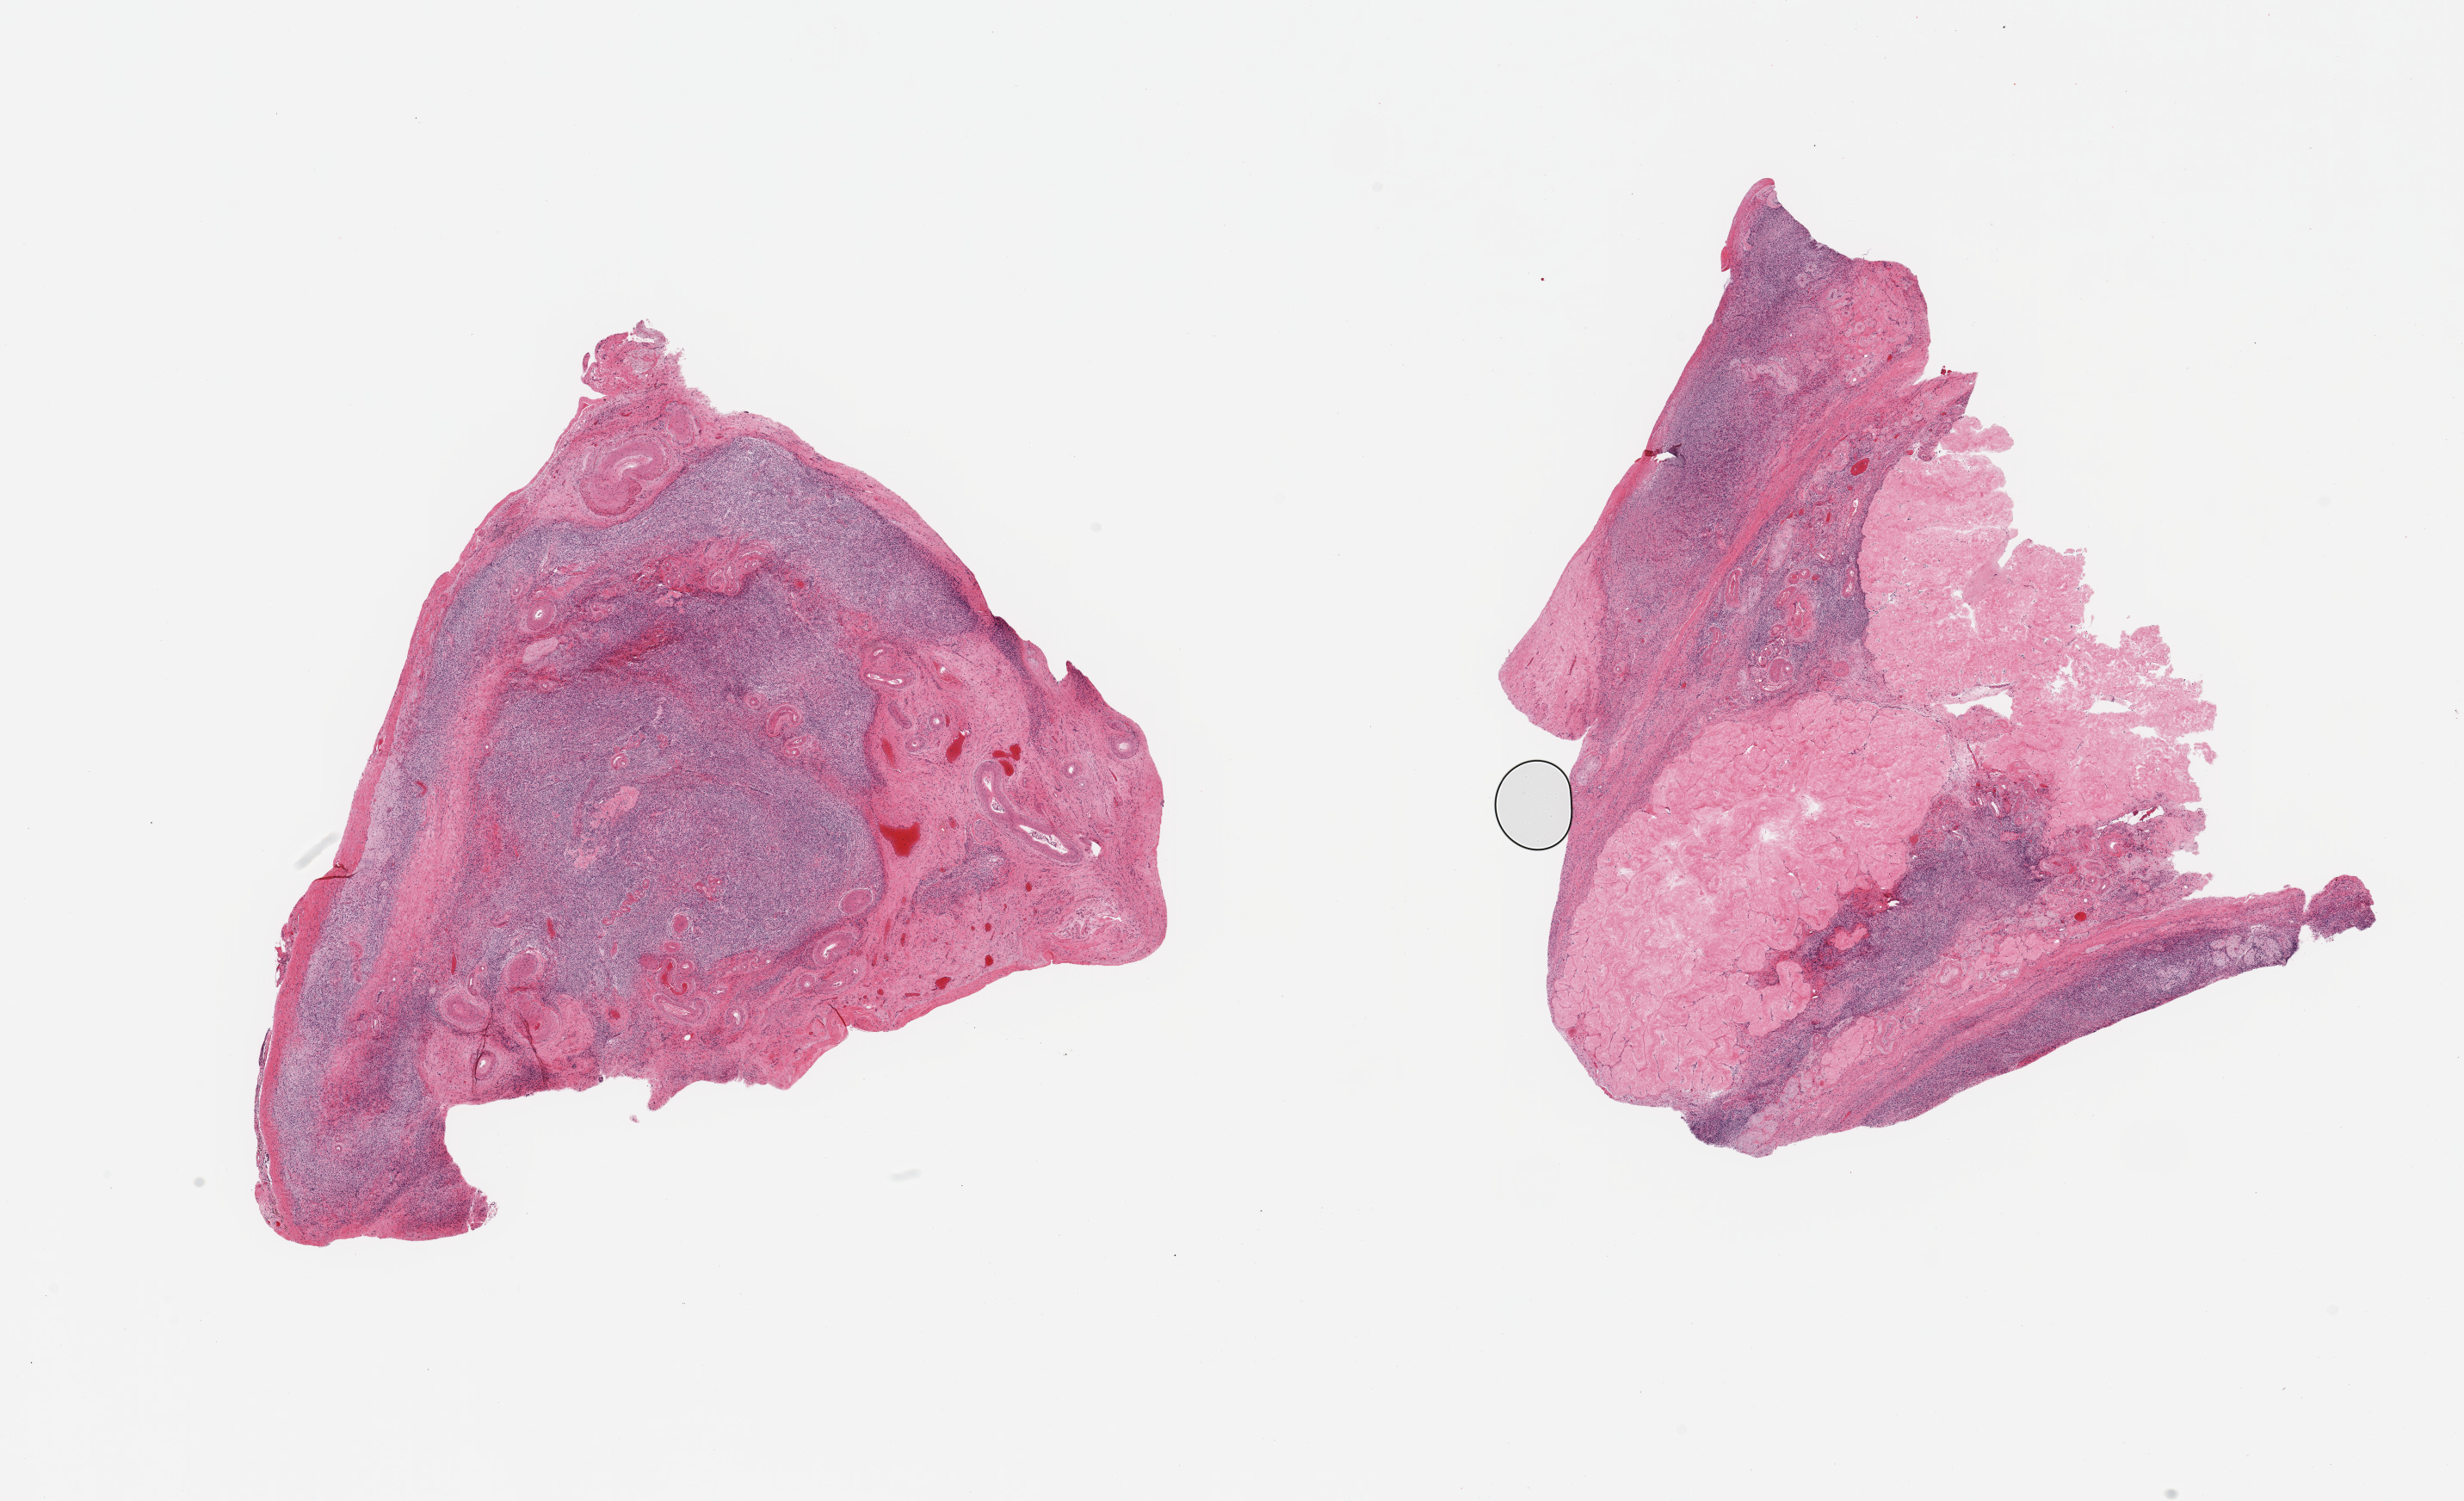
Digitized haematoxylin and eosin-stained section, brightfield, a low-resolution overview of the entire scanned area, about 22.6 x 13.8 mm (acquisition: 20x scan); PAXgene-fixed paraffin-embedded (PFPE) section; target tissue: ovary; donor tissue sample. Donor sex: female.
Reviewer comment on this tissue sample: 2 pieces, atropohic cortex, post menopausal.